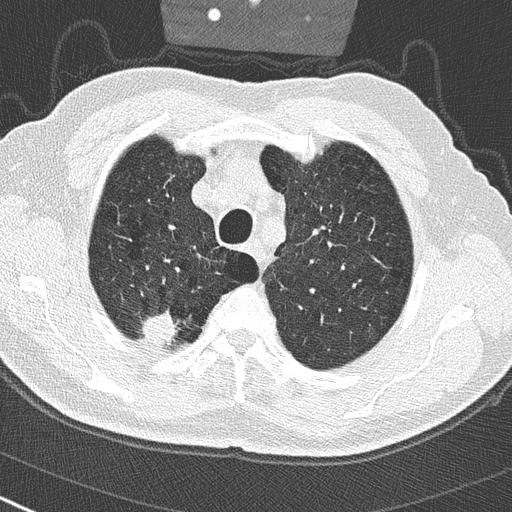
Axial slice from a low-dose chest CT screening exam, baseline annual screen, lung window (W 1500 / L -600 HU), 2 mm slice thickness. Male, age 65 years at enrolment. Current smoker at enrolment.
Lesion marked by an expert reader, bounding box <135,303,186,352> (left, top, right, bottom; pixels). Screening reader's record for this exam (one nodule recorded; not confirmed to be the boxed lesion): non-calcified nodule or mass ≥4 mm, right upper lobe, 24 × 19 mm, spiculated (stellate) margins, soft tissue attenuation. Official screen result: positive, change unspecified: nodule(s) >= 4 mm or enlarging nodule(s), mass(es), or other non-specific abnormalities suspicious for lung cancer.